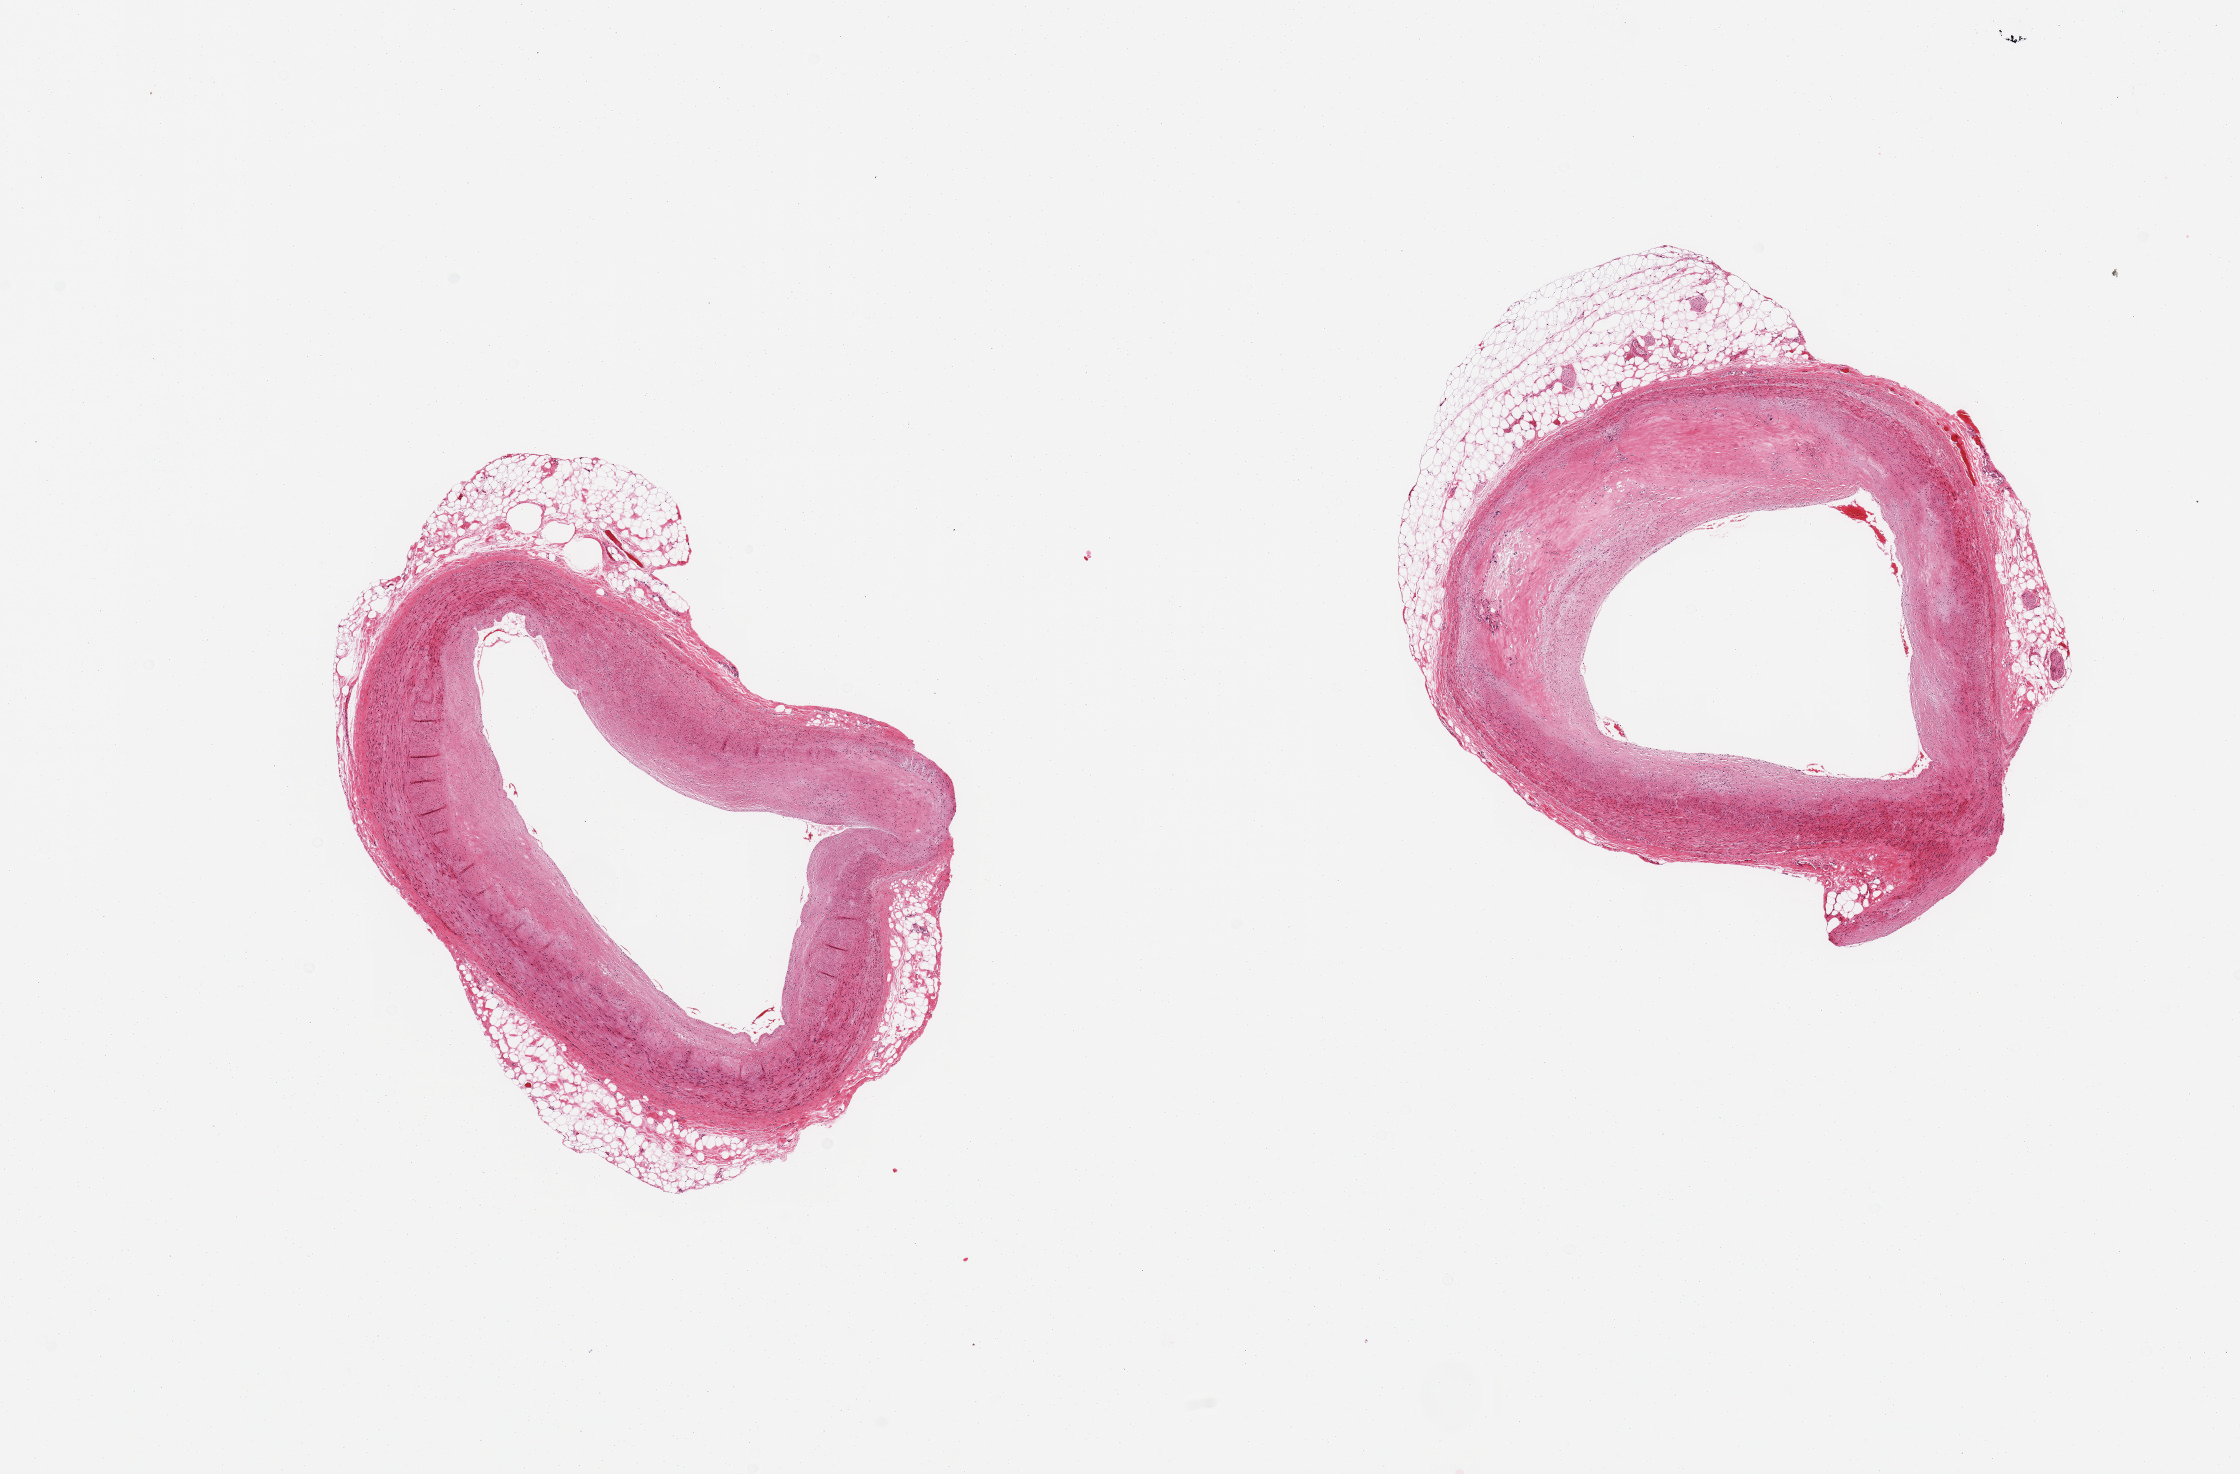
H&E whole-slide image, a low-resolution overview of the entire scanned area, about 17.7 x 11.7 mm (acquisition: 20x scan), PAXgene-fixed paraffin-embedded (PFPE) section, sampled site (target tissue): coronary artery, donor tissue sample. Donor sex: male.
Pathologist's review note for this sample: 2 pieces; thick atherosclerotic intimal plaque with cholesterol clefts; ~25% luminal compromise; over 1mm attached adventitia with fat and nerves.